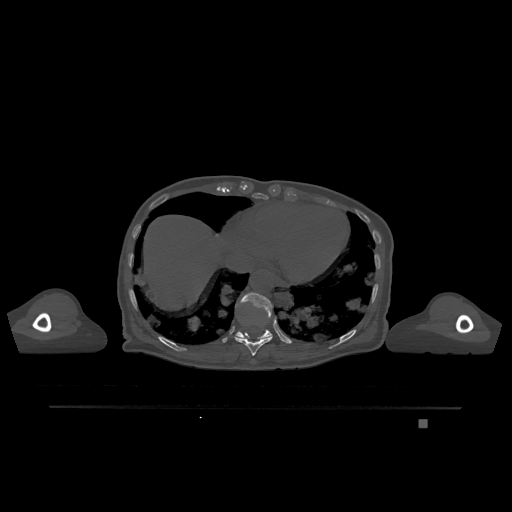
CT including the spine, one axial slice. Position 623 of 1317 along the scan axis. Bone window (W 1800 / L 400 HU). 0.5 mm slice thickness. 512 × 512 image matrix, field of view 500 × 500 mm. Female patient, age 74 years. From the clinical record (not read from this slice): primary cancer: lung; vertebrae with lytic lesions (as recorded): T1, T4, T5, T6, L4, L5.
Annotated regions visible in this slice (semi-automatically segmented with operator editing):
- T10 vertebra: bounding box <235,333,273,356> (left, top, right, bottom; pixels)
- T11 vertebra: <235,292,273,339>